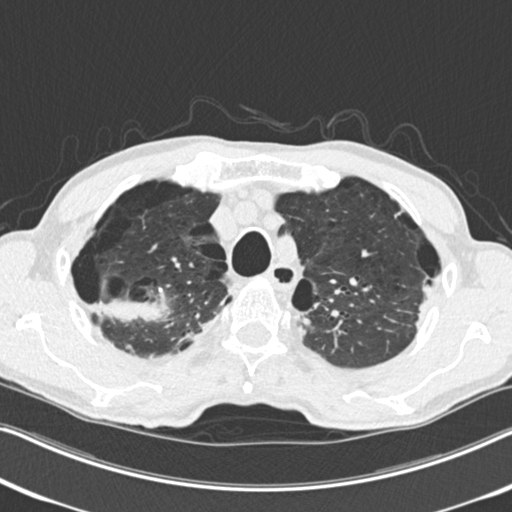
Low-dose screening chest CT, one axial slice; position 201 of 251 along the scan axis; reconstruction kernel B30f; 120 kVp; lung window (W 1500 / L -600 HU); 512 × 512 image matrix, field of view 334 × 334 mm.
Annotated regions visible in this slice (manually delineated by an expert):
- lesion 1 (tumor, upper lobe of right lung): bounding box (x1, y1, x2, y2) in pixels: (88, 300, 161, 321)